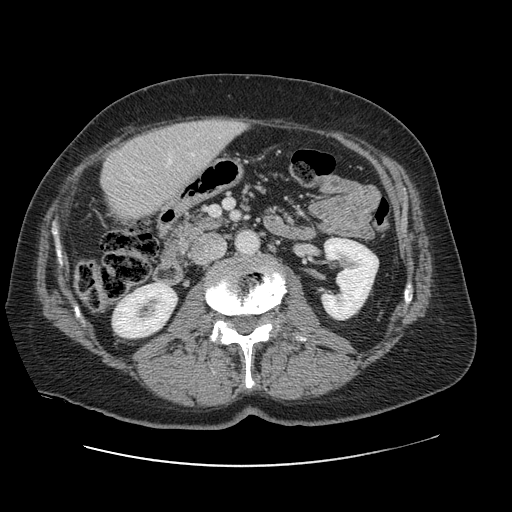
Contrast-enhanced abdominal CT, one axial slice; position 27 of 138 along the scan axis; intravenous contrast given; soft-tissue window (W 400 / L 40 HU); 2.5 mm slice thickness; 512 × 512 image matrix, field of view 402 × 402 mm. Male patient, age 71 years. Case-level facts recorded for this patient, not image findings: diagnosis: colorectal cancer liver metastases, imaged before liver resection; multiple liver metastases: no; largest metastasis: 3.3 cm; disease in both lobes: no.
Outlined on this slice (outlined manually by an expert reader):
- liver: bounding box <102,119,246,220> (left, top, right, bottom; pixels)
- planned liver remnant (the part of the liver to remain after resection): <101,133,180,219>
- portal vein (with intrahepatic branches): <169,160,171,163>